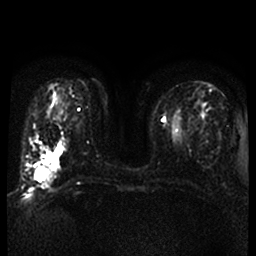
Breast MRI, one axial slice; slice 16 of 52 in the series (ordered by position); diffusion-weighted series; image 2 of 4 stored at this slice position (different b-values; order by instance number); 1.5 T; 4 mm slice thickness; 256 × 256 image matrix, field of view 320 × 320 mm. Female patient.
Outlined on this slice (outlined manually by an expert reader):
- tumour on diffusion-weighted imaging: bounding box [x1, y1, x2, y2] px = [35, 155, 52, 183]